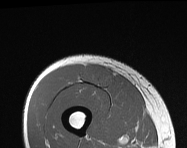
MRI of an extremity soft-tissue mass, one axial slice. Position 44 of 114 along the scan axis. MR volume resampled by the dataset authors to the PET/CT grid (not the native acquisition matrix). 187 × 148 image matrix, field of view 183 × 145 mm. Male patient. From the clinical record (not read from this slice): histological type: pleiomorphic leiomyosarcoma; grade: intermediate; site of the primary tumour: right thigh.
Outlined on this slice (expert contour drawn on MRI and transferred to this co-registered scan by the dataset authors):
- gross tumour volume including surrounding oedema: box from (x=82, y=65) to (x=113, y=87) px